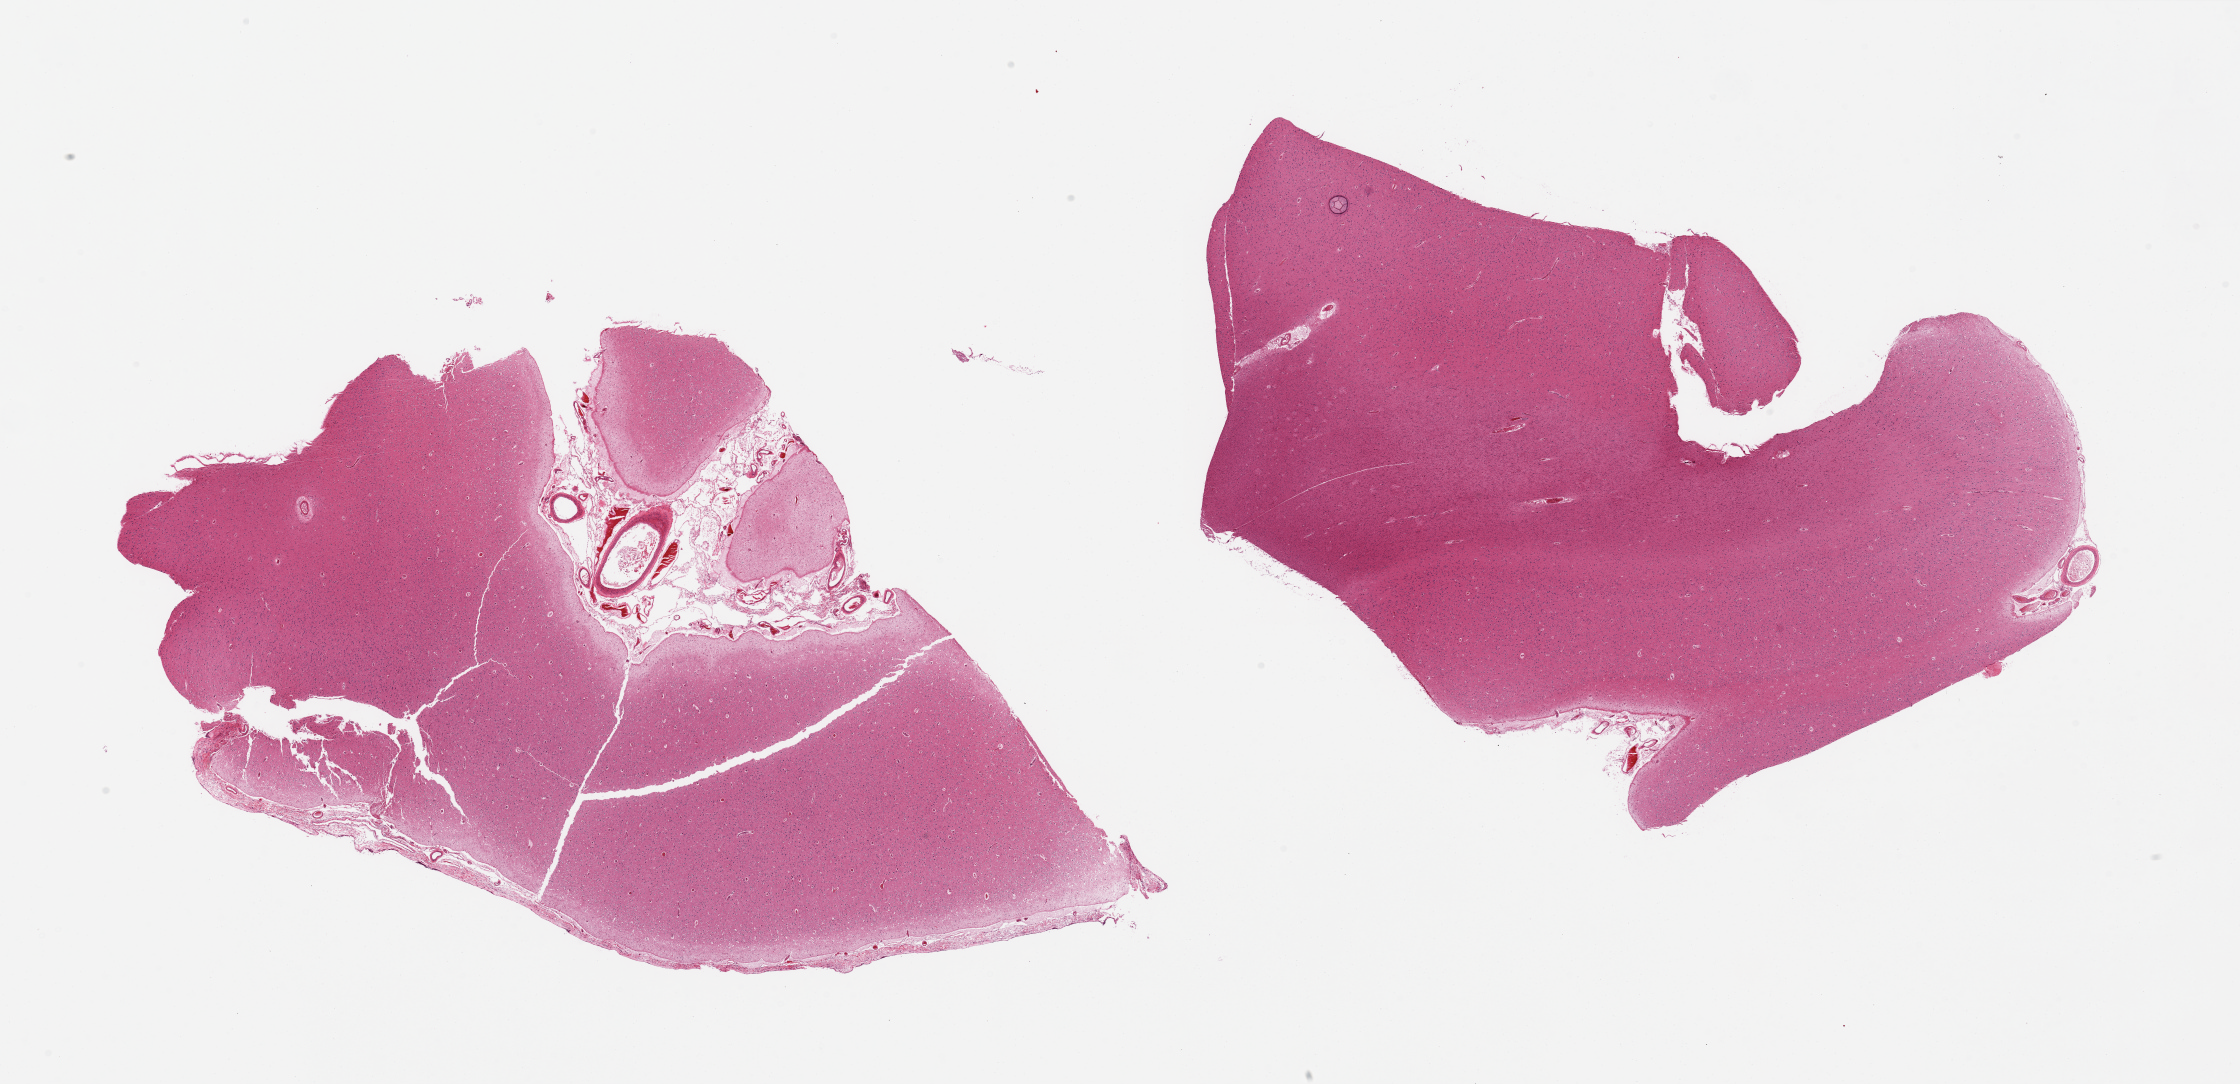
Haematoxylin and eosin whole-slide image, brightfield, low-resolution overview of the scanned area, about 35.4 x 17.2 mm (acquisition: 20x scan); PAXgene-fixed, paraffin-embedded tissue; target tissue: cerebral cortex; donor tissue sample.
Reviewer comment on this tissue sample: 2 pieces, no abnormalities.